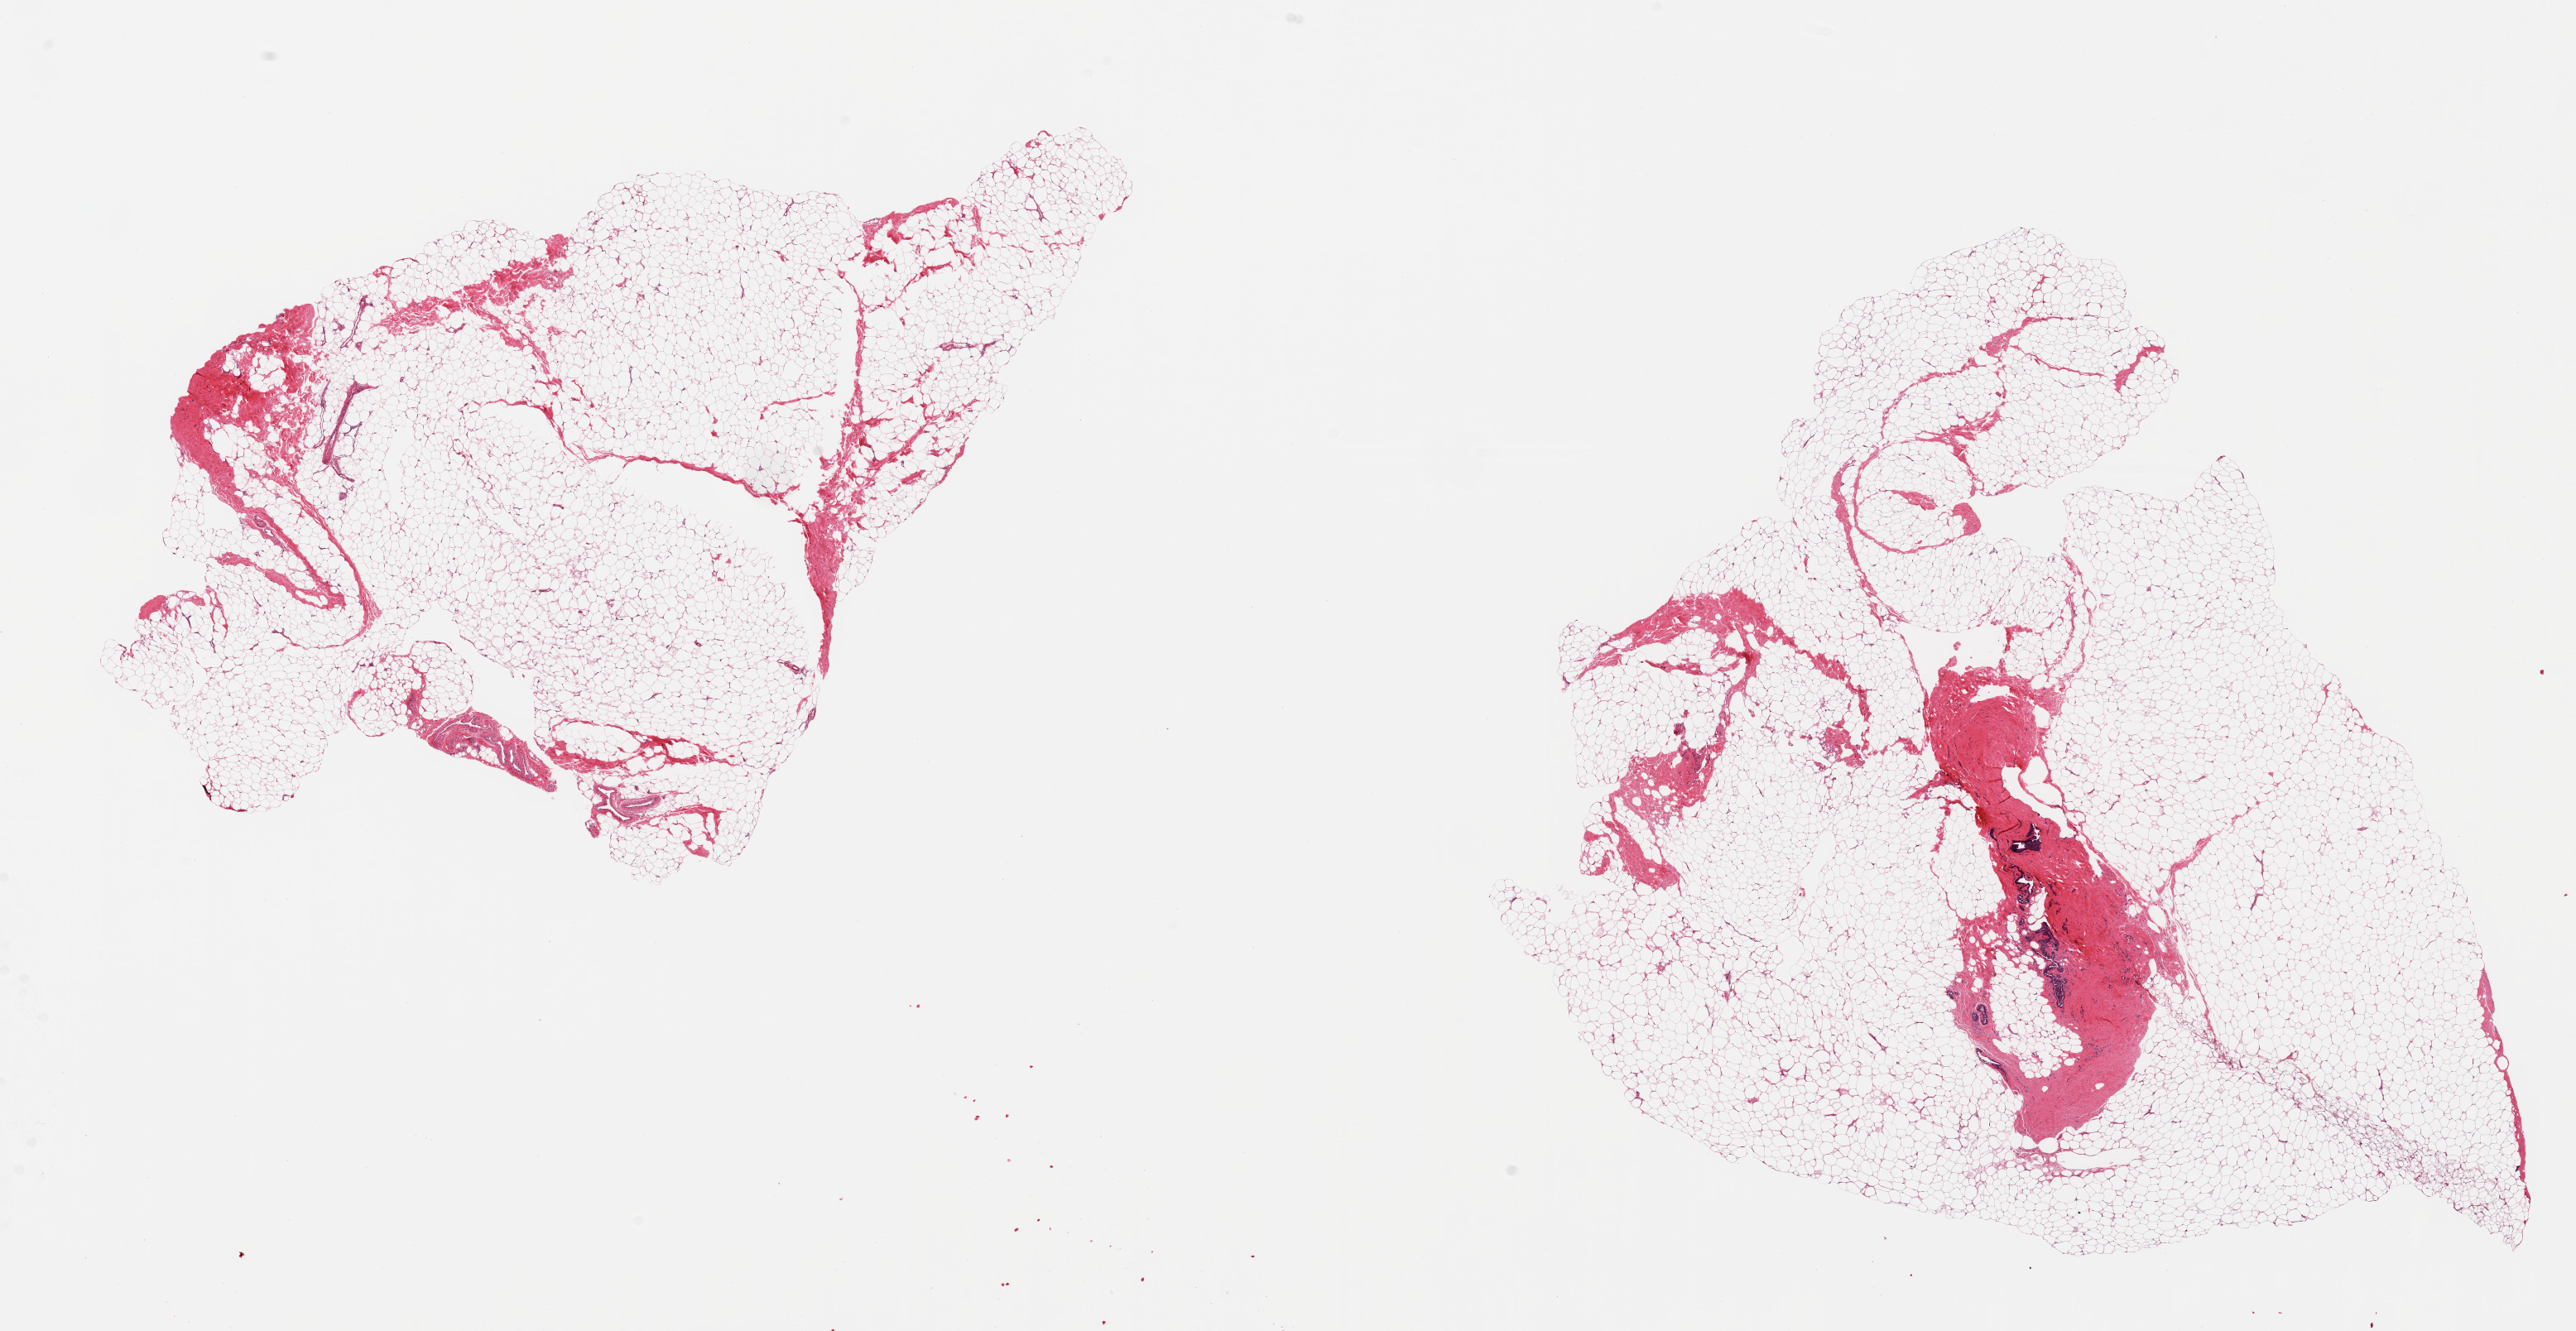
Whole-slide image, H&E stain, brightfield, whole scanned area (about 24.6 x 12.7 mm) shown as a low-resolution overview. PAXgene-fixed paraffin-embedded (PFPE) section. Sampled site (target tissue): breast. Donor tissue sample.
• review note (as recorded): 2 pieces; >80% mature adipose tissue; one piece contains ductal structures embedded in dense fibrotic stroma